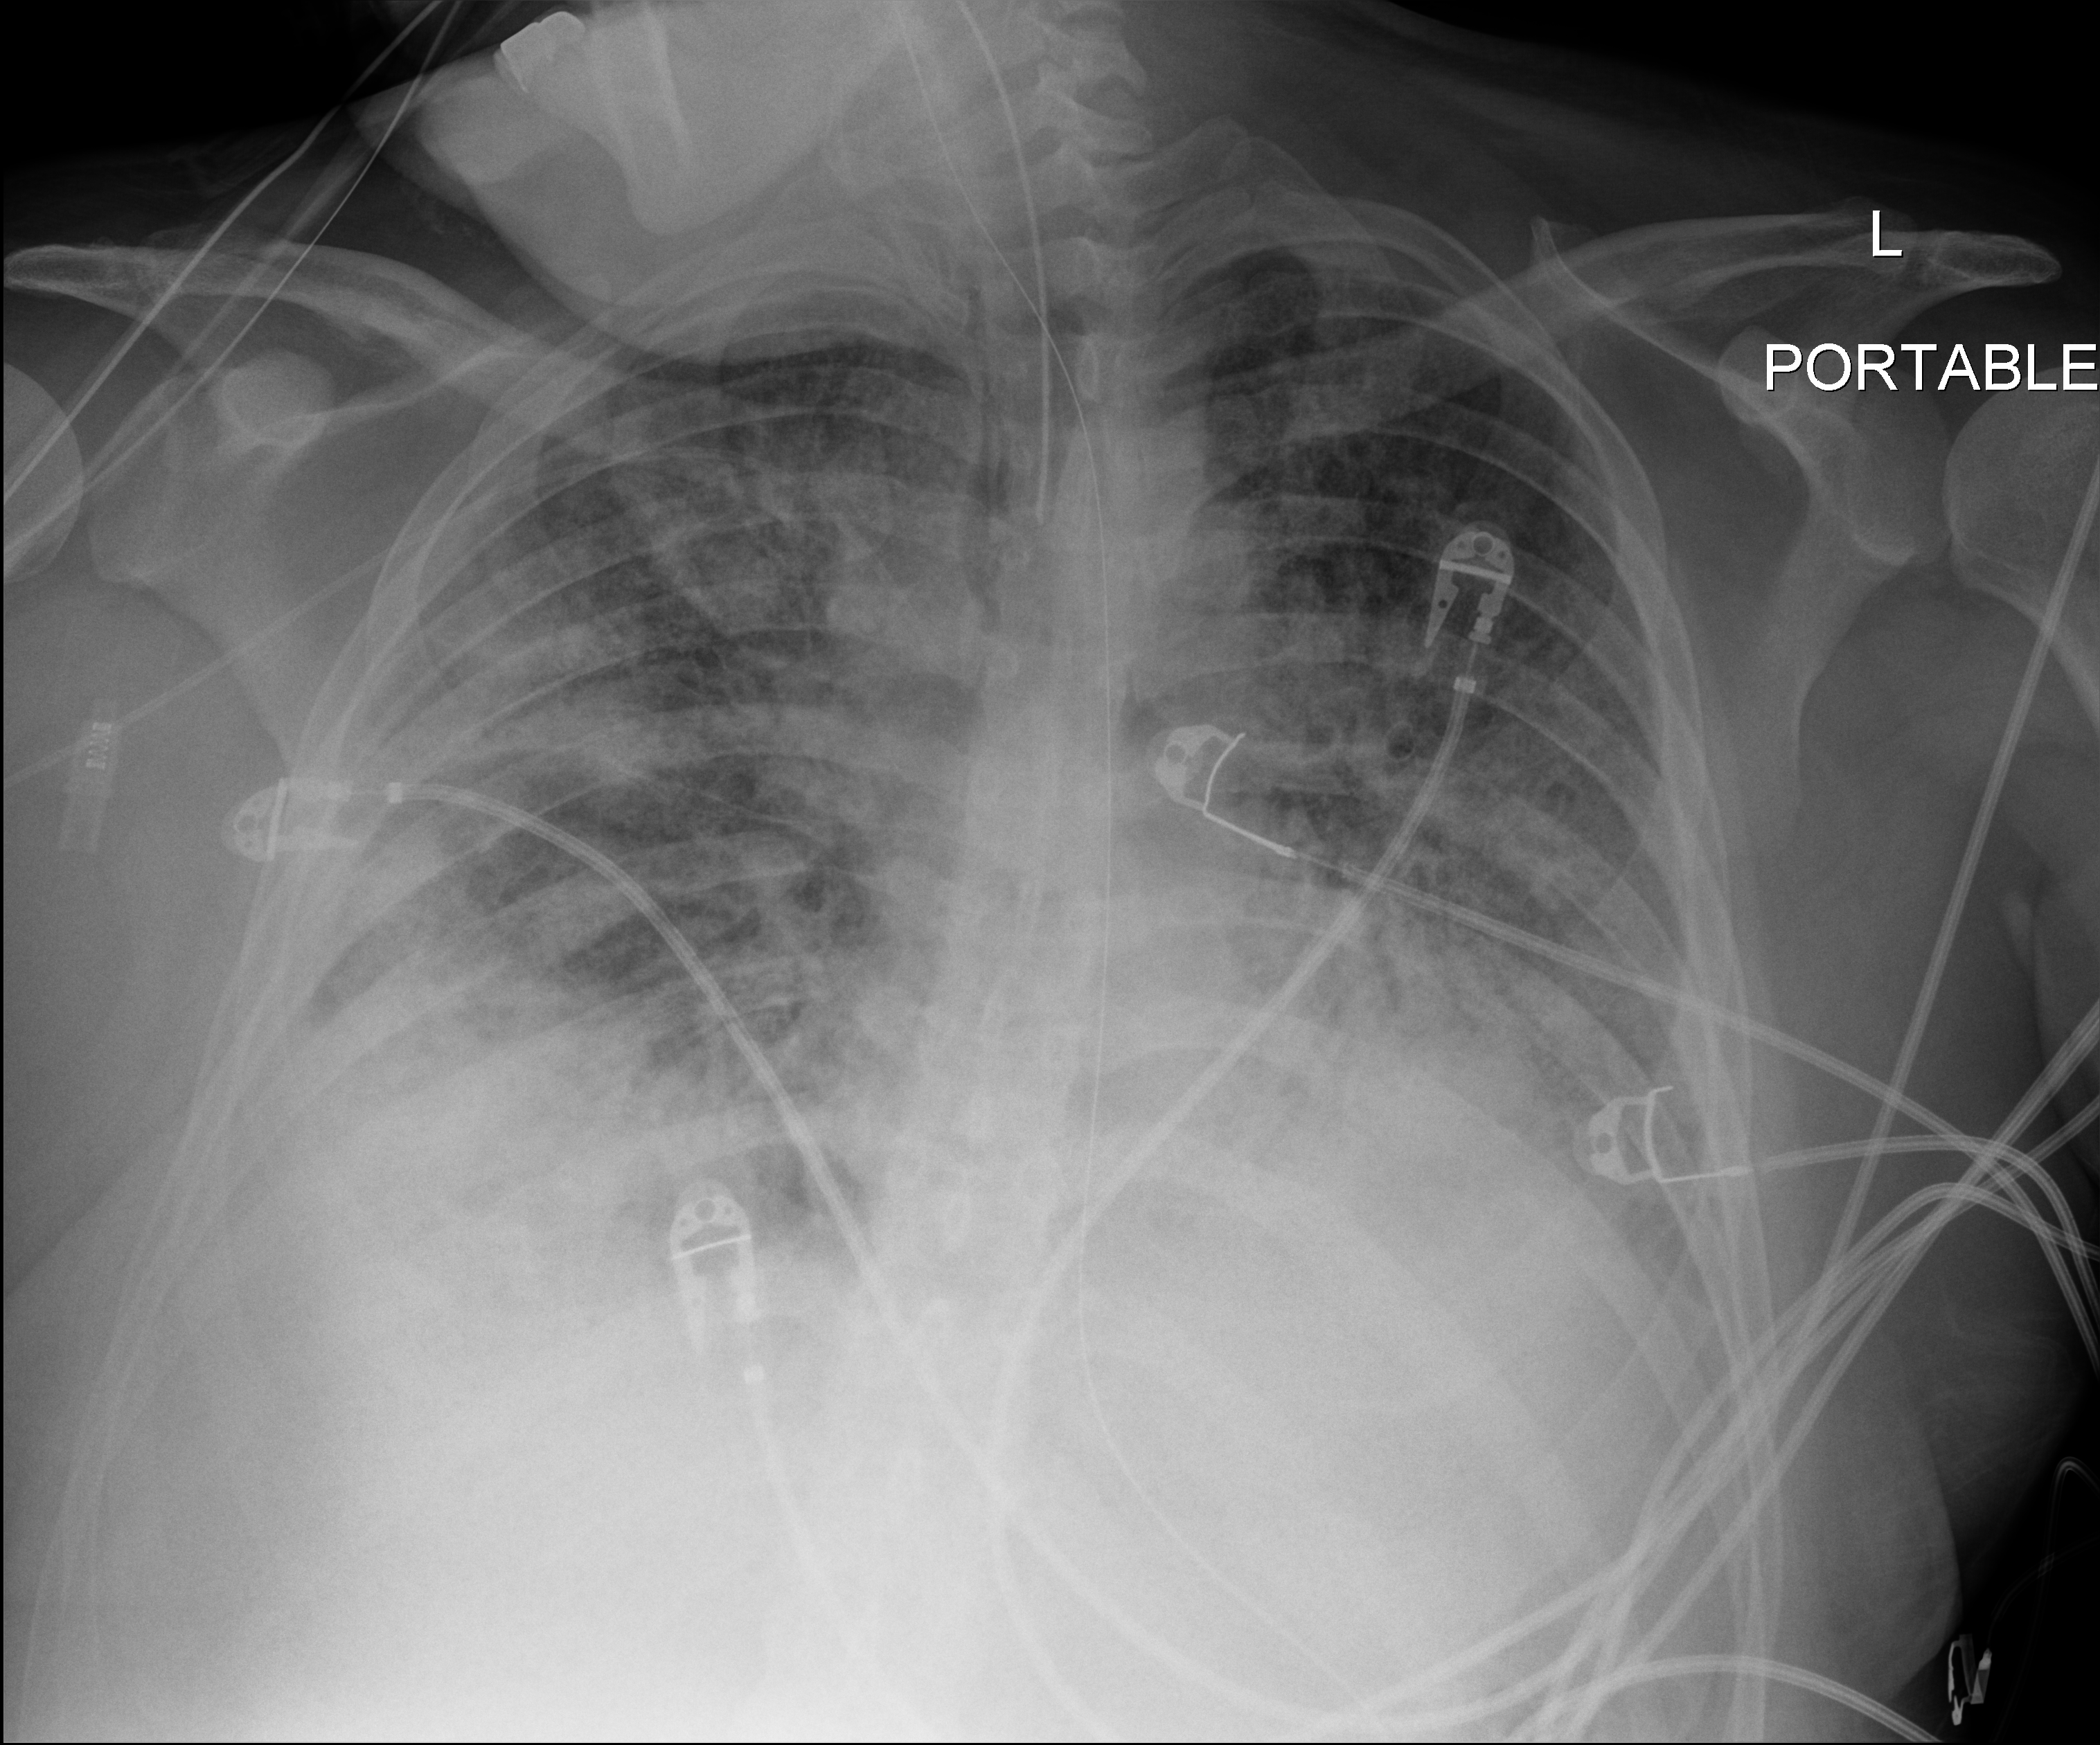
Bedside chest radiograph (digital radiography); anteroposterior (AP) projection. Patient hospitalised with COVID-19; male, aged 18–59 years.
From the hospital-stay record, not from the radiograph (when in the stay this image was taken is not recorded): admitted to intensive care during this hospital stay: yes.